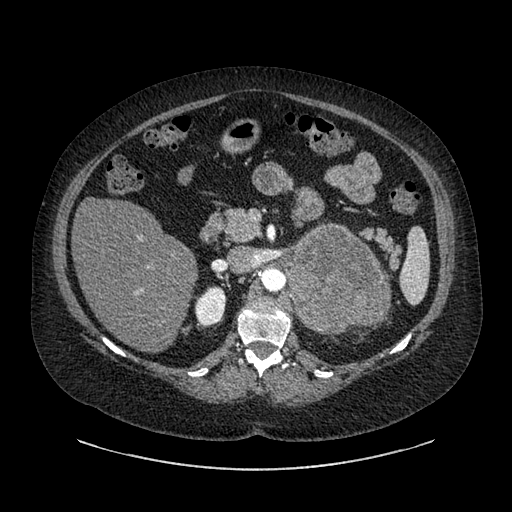
Contrast-enhanced abdominal CT, one axial slice. Intravenous contrast given. Soft-tissue window (W 400 / L 40 HU). 0.62 mm slice thickness. 512 × 512 image matrix, field of view 460 × 460 mm. Patient: female, 61 years. Case-level facts recorded for this patient, not image findings: diagnosis: adrenocortical carcinoma; tumour side: left adrenal; tumour size at pathology: 13 cm; Ki-67 index: 79 %; stage (as recorded): 2.
Annotated regions visible in this slice (semi-automatic segmentation, software-assisted and operator-edited):
- mass: bounding box <289,227,387,334> (left, top, right, bottom; pixels)